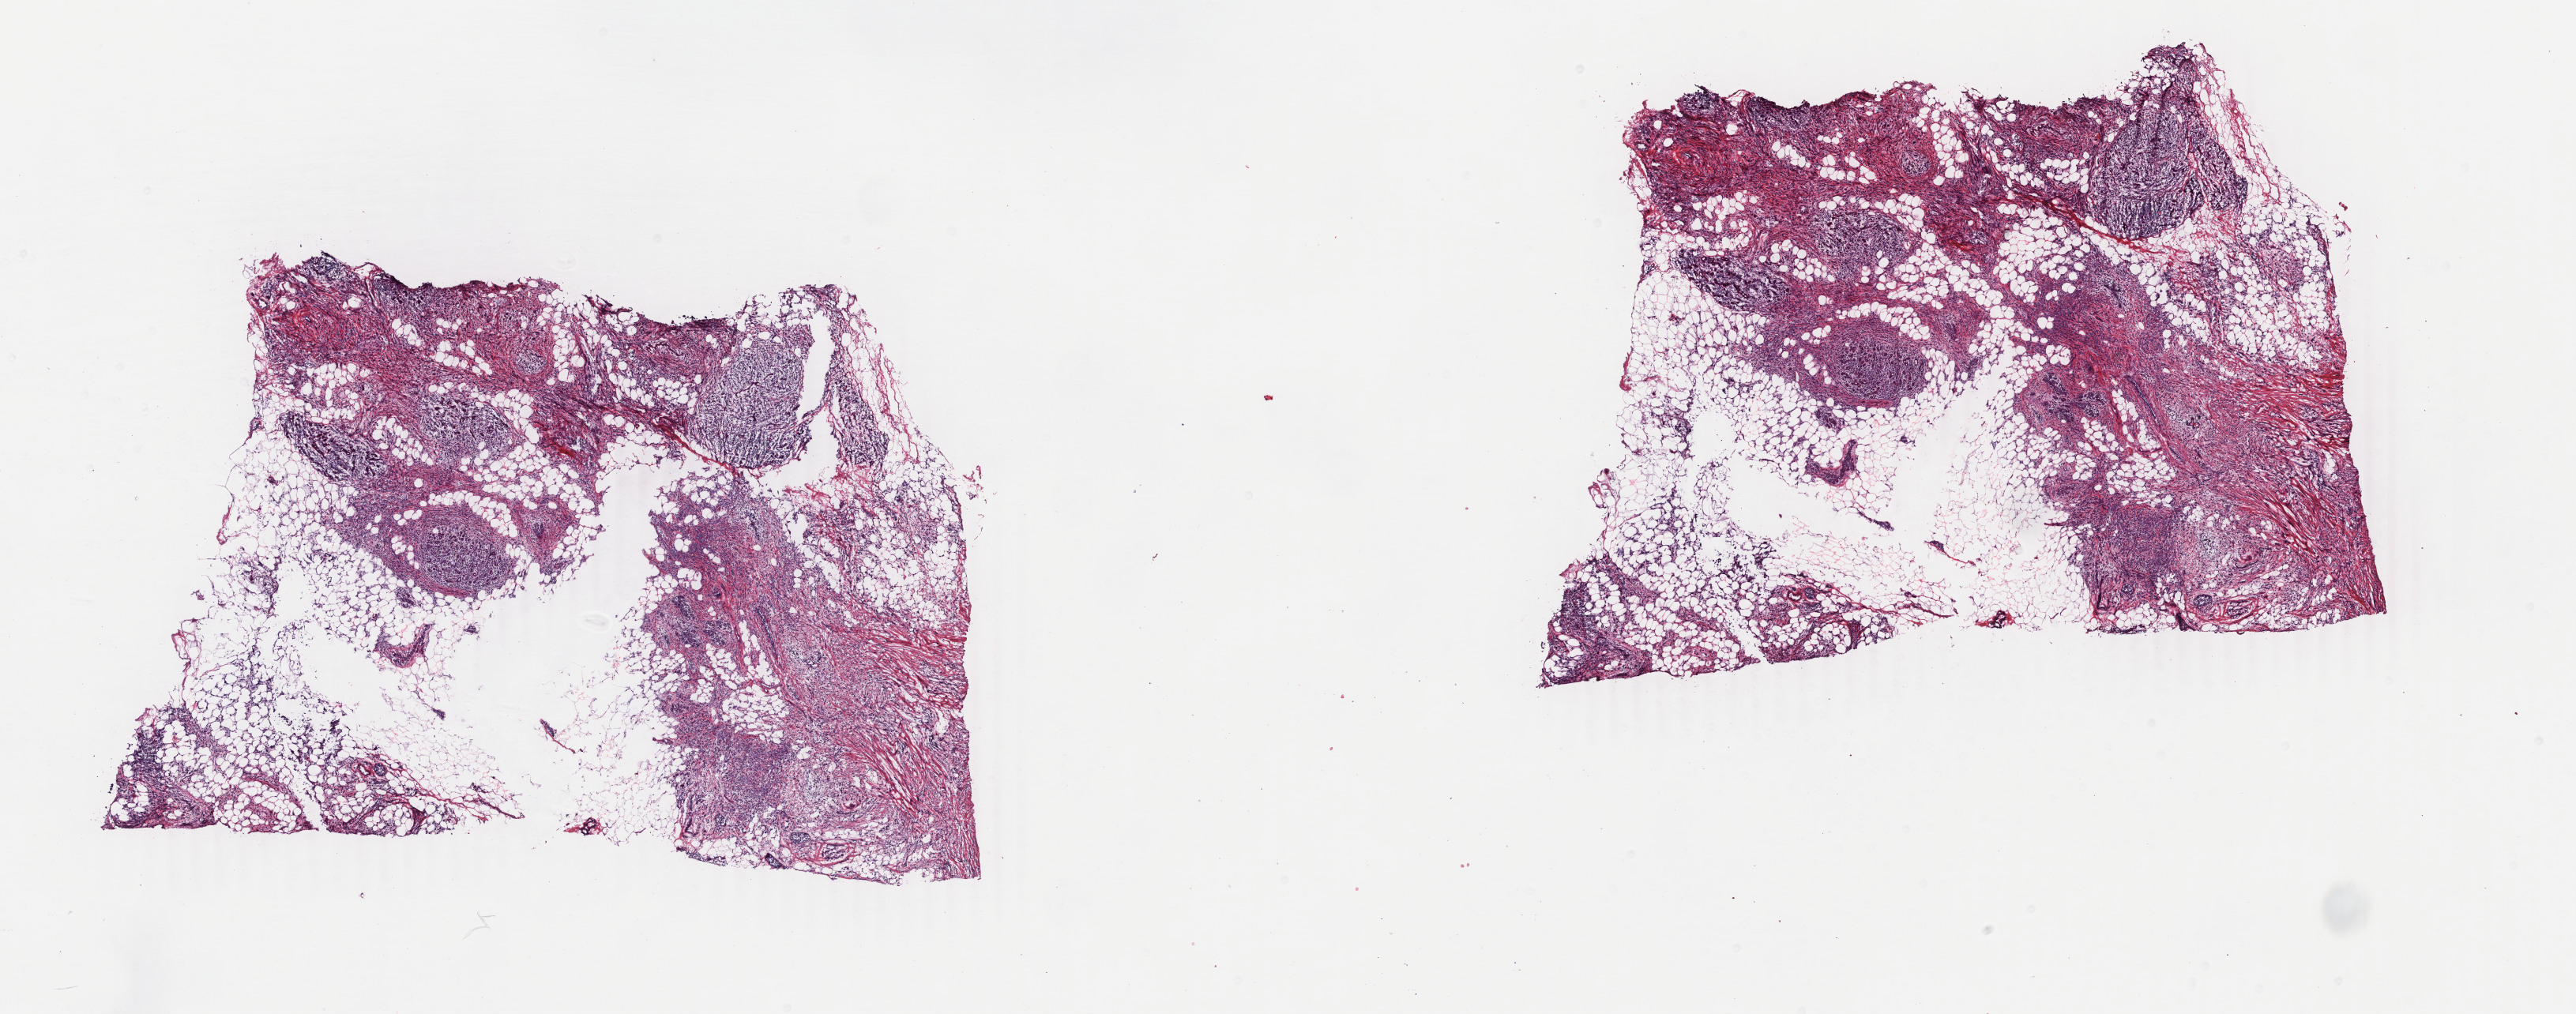
Digitized H&E-stained tissue section (whole slide) — low-resolution overview of the scanned area, about 25.9 x 10.2 mm (slide scanned at 40x). Frozen section from the top of the tissue portion. Breast, primary tumour sample. Female patient; age at initial diagnosis 54 years. Composition of this section per pathologist review: tumour cells 80%, tumour nuclei 65%.
Pathologic diagnosis: Lobular carcinoma, NOS.